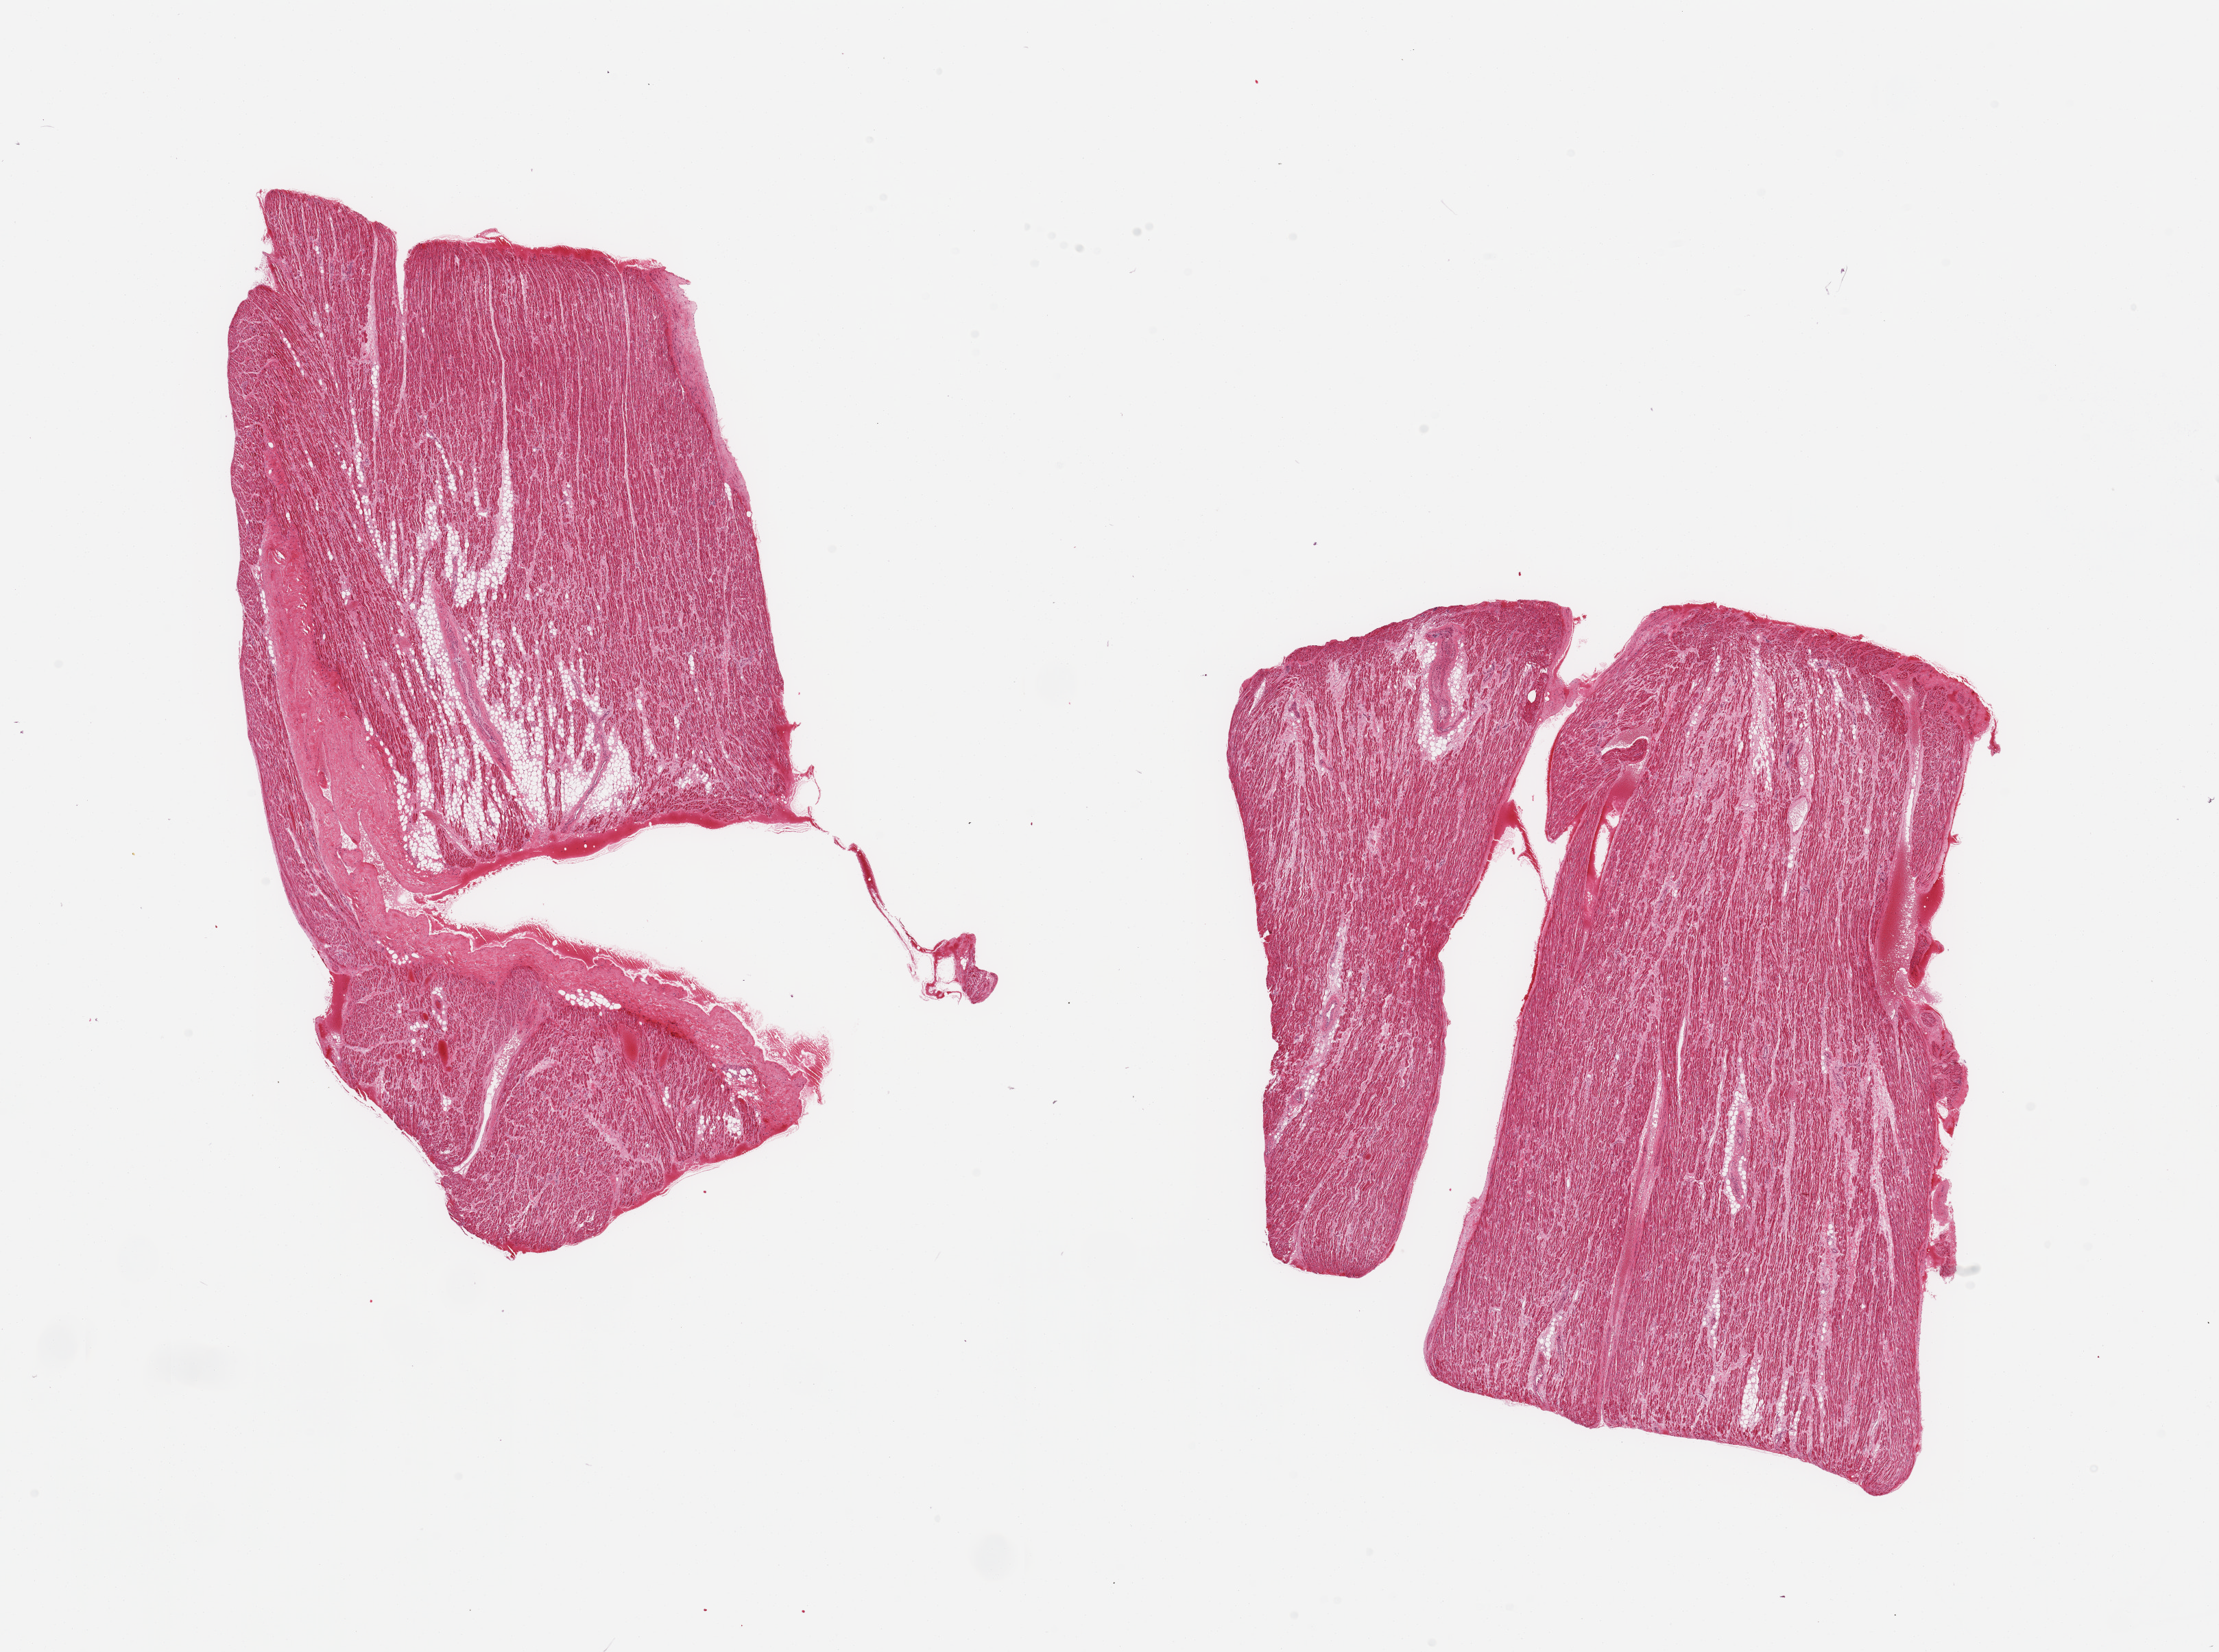
Whole-slide image, haematoxylin and eosin stain, low-resolution overview of the scanned area, about 25.6 x 19.1 mm (acquisition: 20x scan), PAXgene-fixed paraffin-embedded (PFPE) section, section of auricular appendage (target tissue), donor tissue sample. Donor: male.
Review note (as recorded): 2 pieces; ~10% interstitial fat; congestion.